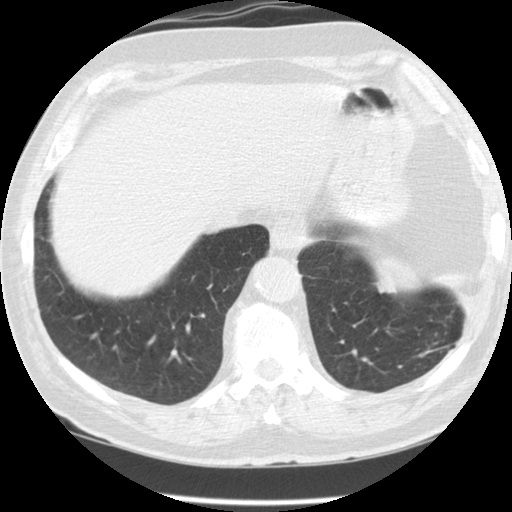
Low-dose screening chest CT, one axial slice; slice 31 of 127 in the series (ordered by position); reconstruction kernel STANDARD; lung window (W 1500 / L -600 HU); 2.5 mm slice thickness; 512 × 512 image matrix.
Annotated regions visible in this slice (manually delineated by an expert):
- lesion 1 (tumor, lower lobe of left lung): bounding box [x1, y1, x2, y2] px = [376, 281, 396, 293]